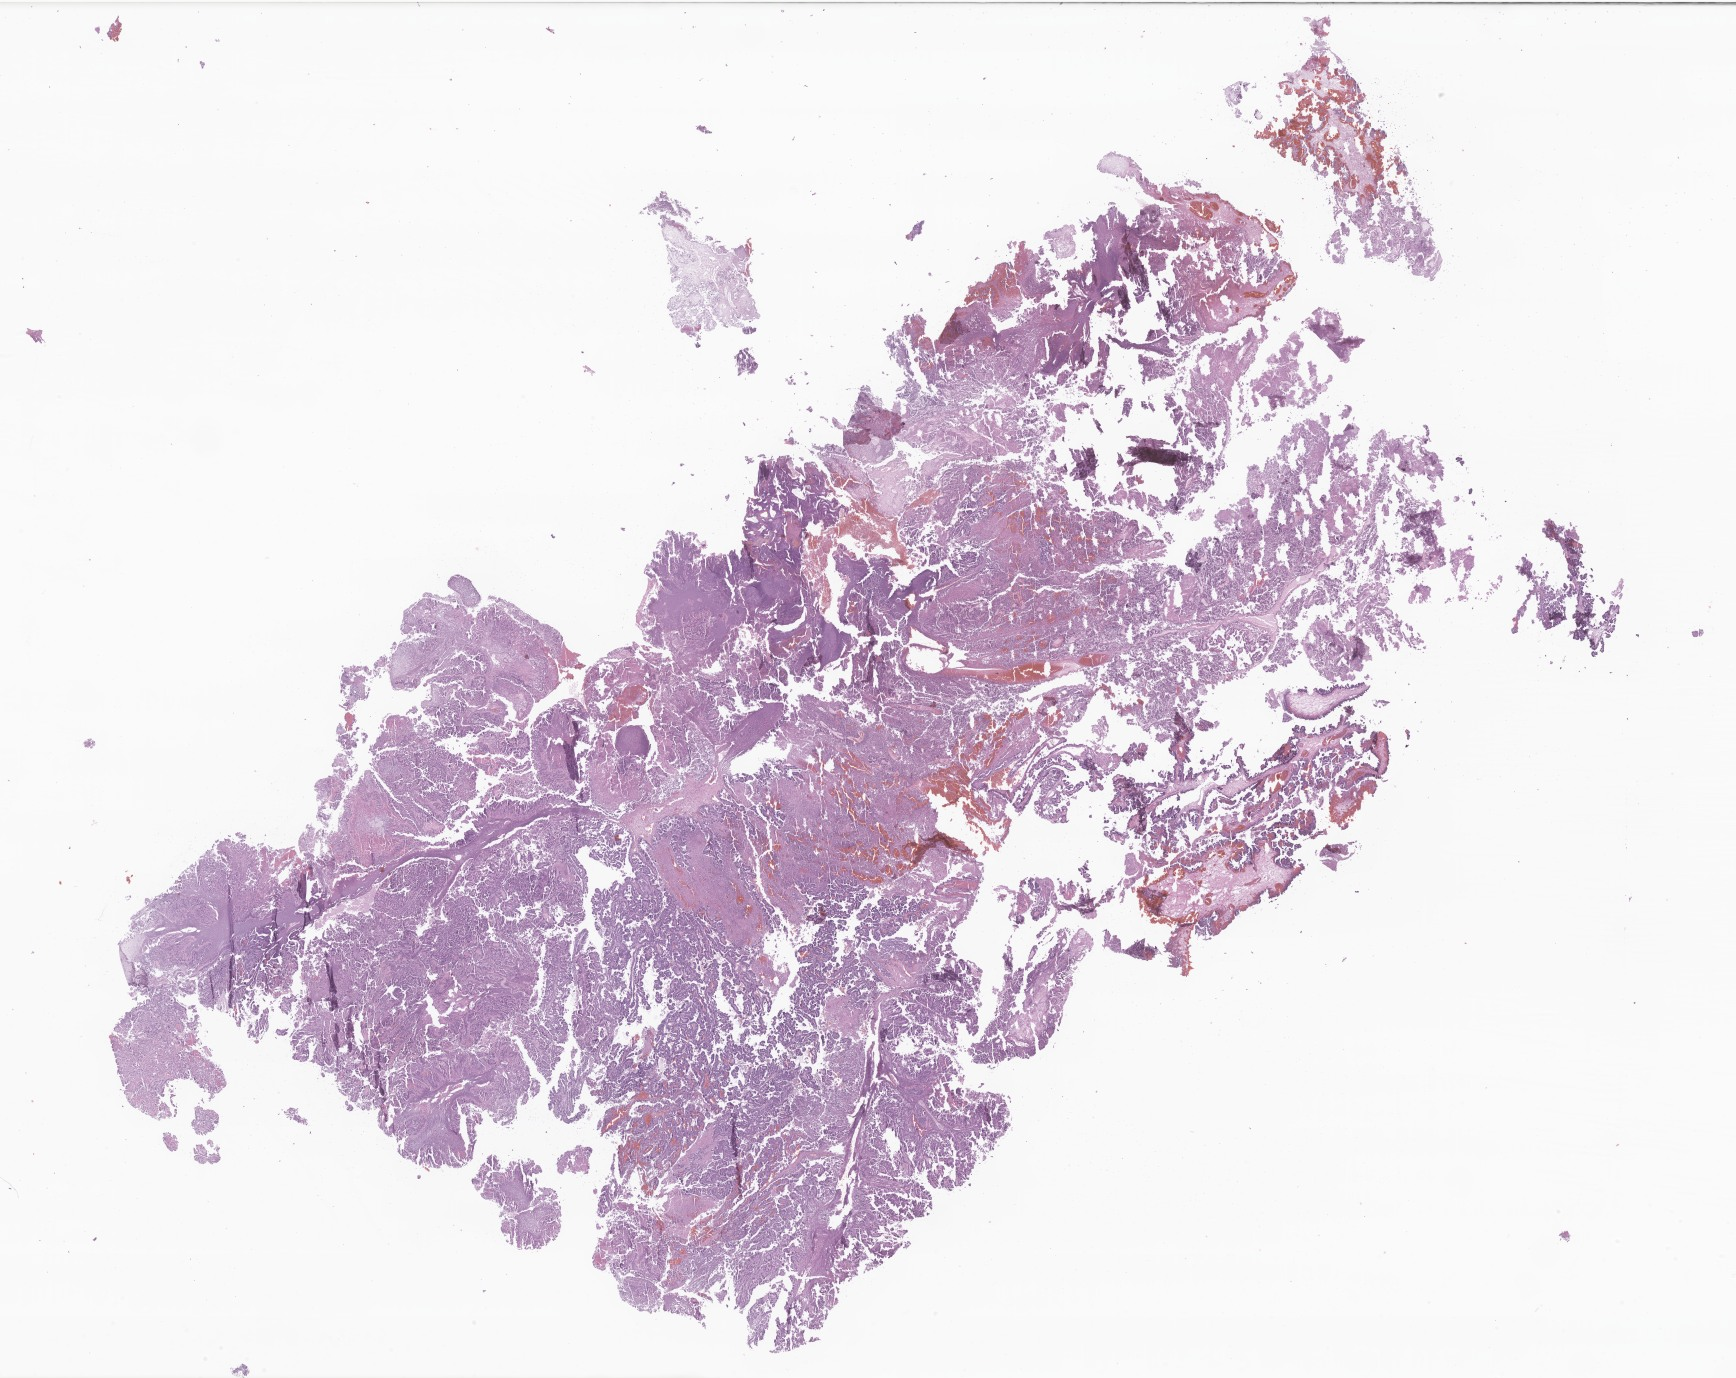
Digitized hematoxylin and eosin (H&E)-stained section of tumor tissue from the brain, whole scanned area (about 29.3 x 23.2 mm) shown as a low-resolution overview, formalin-fixed paraffin-embedded section. Patient: female, age 218 days.
Recorded diagnosis: Choroid plexus papilloma, NOS.